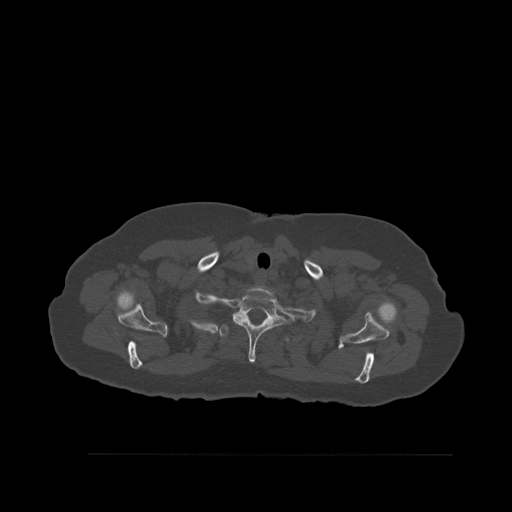
CT including the spine, one axial slice; slice 442 of 527 in the series (ordered by position); bone window (W 1800 / L 400 HU); 512 × 512 image matrix, field of view 470 × 470 mm. Patient: female, 73 years. Case-level facts recorded for this patient, not image findings: primary cancer: breast; vertebrae with lytic lesions (as recorded): L2.
Outlined on this slice (semi-automatically segmented with operator editing):
- T1 vertebra: box from (x=233, y=293) to (x=288, y=363) px
- T2 vertebra: (x=222, y=321)–(x=289, y=343)